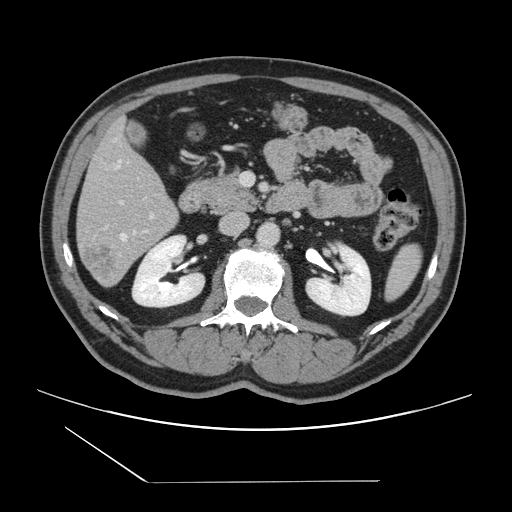
Contrast-enhanced abdominal CT, one axial slice. Position 60 of 157 along the scan axis. Intravenous contrast given. Soft-tissue window (W 400 / L 40 HU). 2.5 mm slice thickness. 512 × 512 image matrix, field of view 407 × 407 mm. Male patient, age 61 years. From the clinical record (not read from this slice): diagnosis: colorectal cancer liver metastases, imaged before liver resection; multiple liver metastases: yes; largest metastasis: 5.5 cm; chemotherapy before resection: no.
Structures marked on this image (expert manual segmentation):
- hepatic veins: bounding box (x1, y1, x2, y2) in pixels: (117, 160, 135, 240)
- liver: (77, 122, 178, 286)
- planned liver remnant (the part of the liver to remain after resection): (78, 122, 170, 218)
- portal vein (with intrahepatic branches): (105, 201, 154, 228)
- liver metastasis: (82, 243, 122, 284)